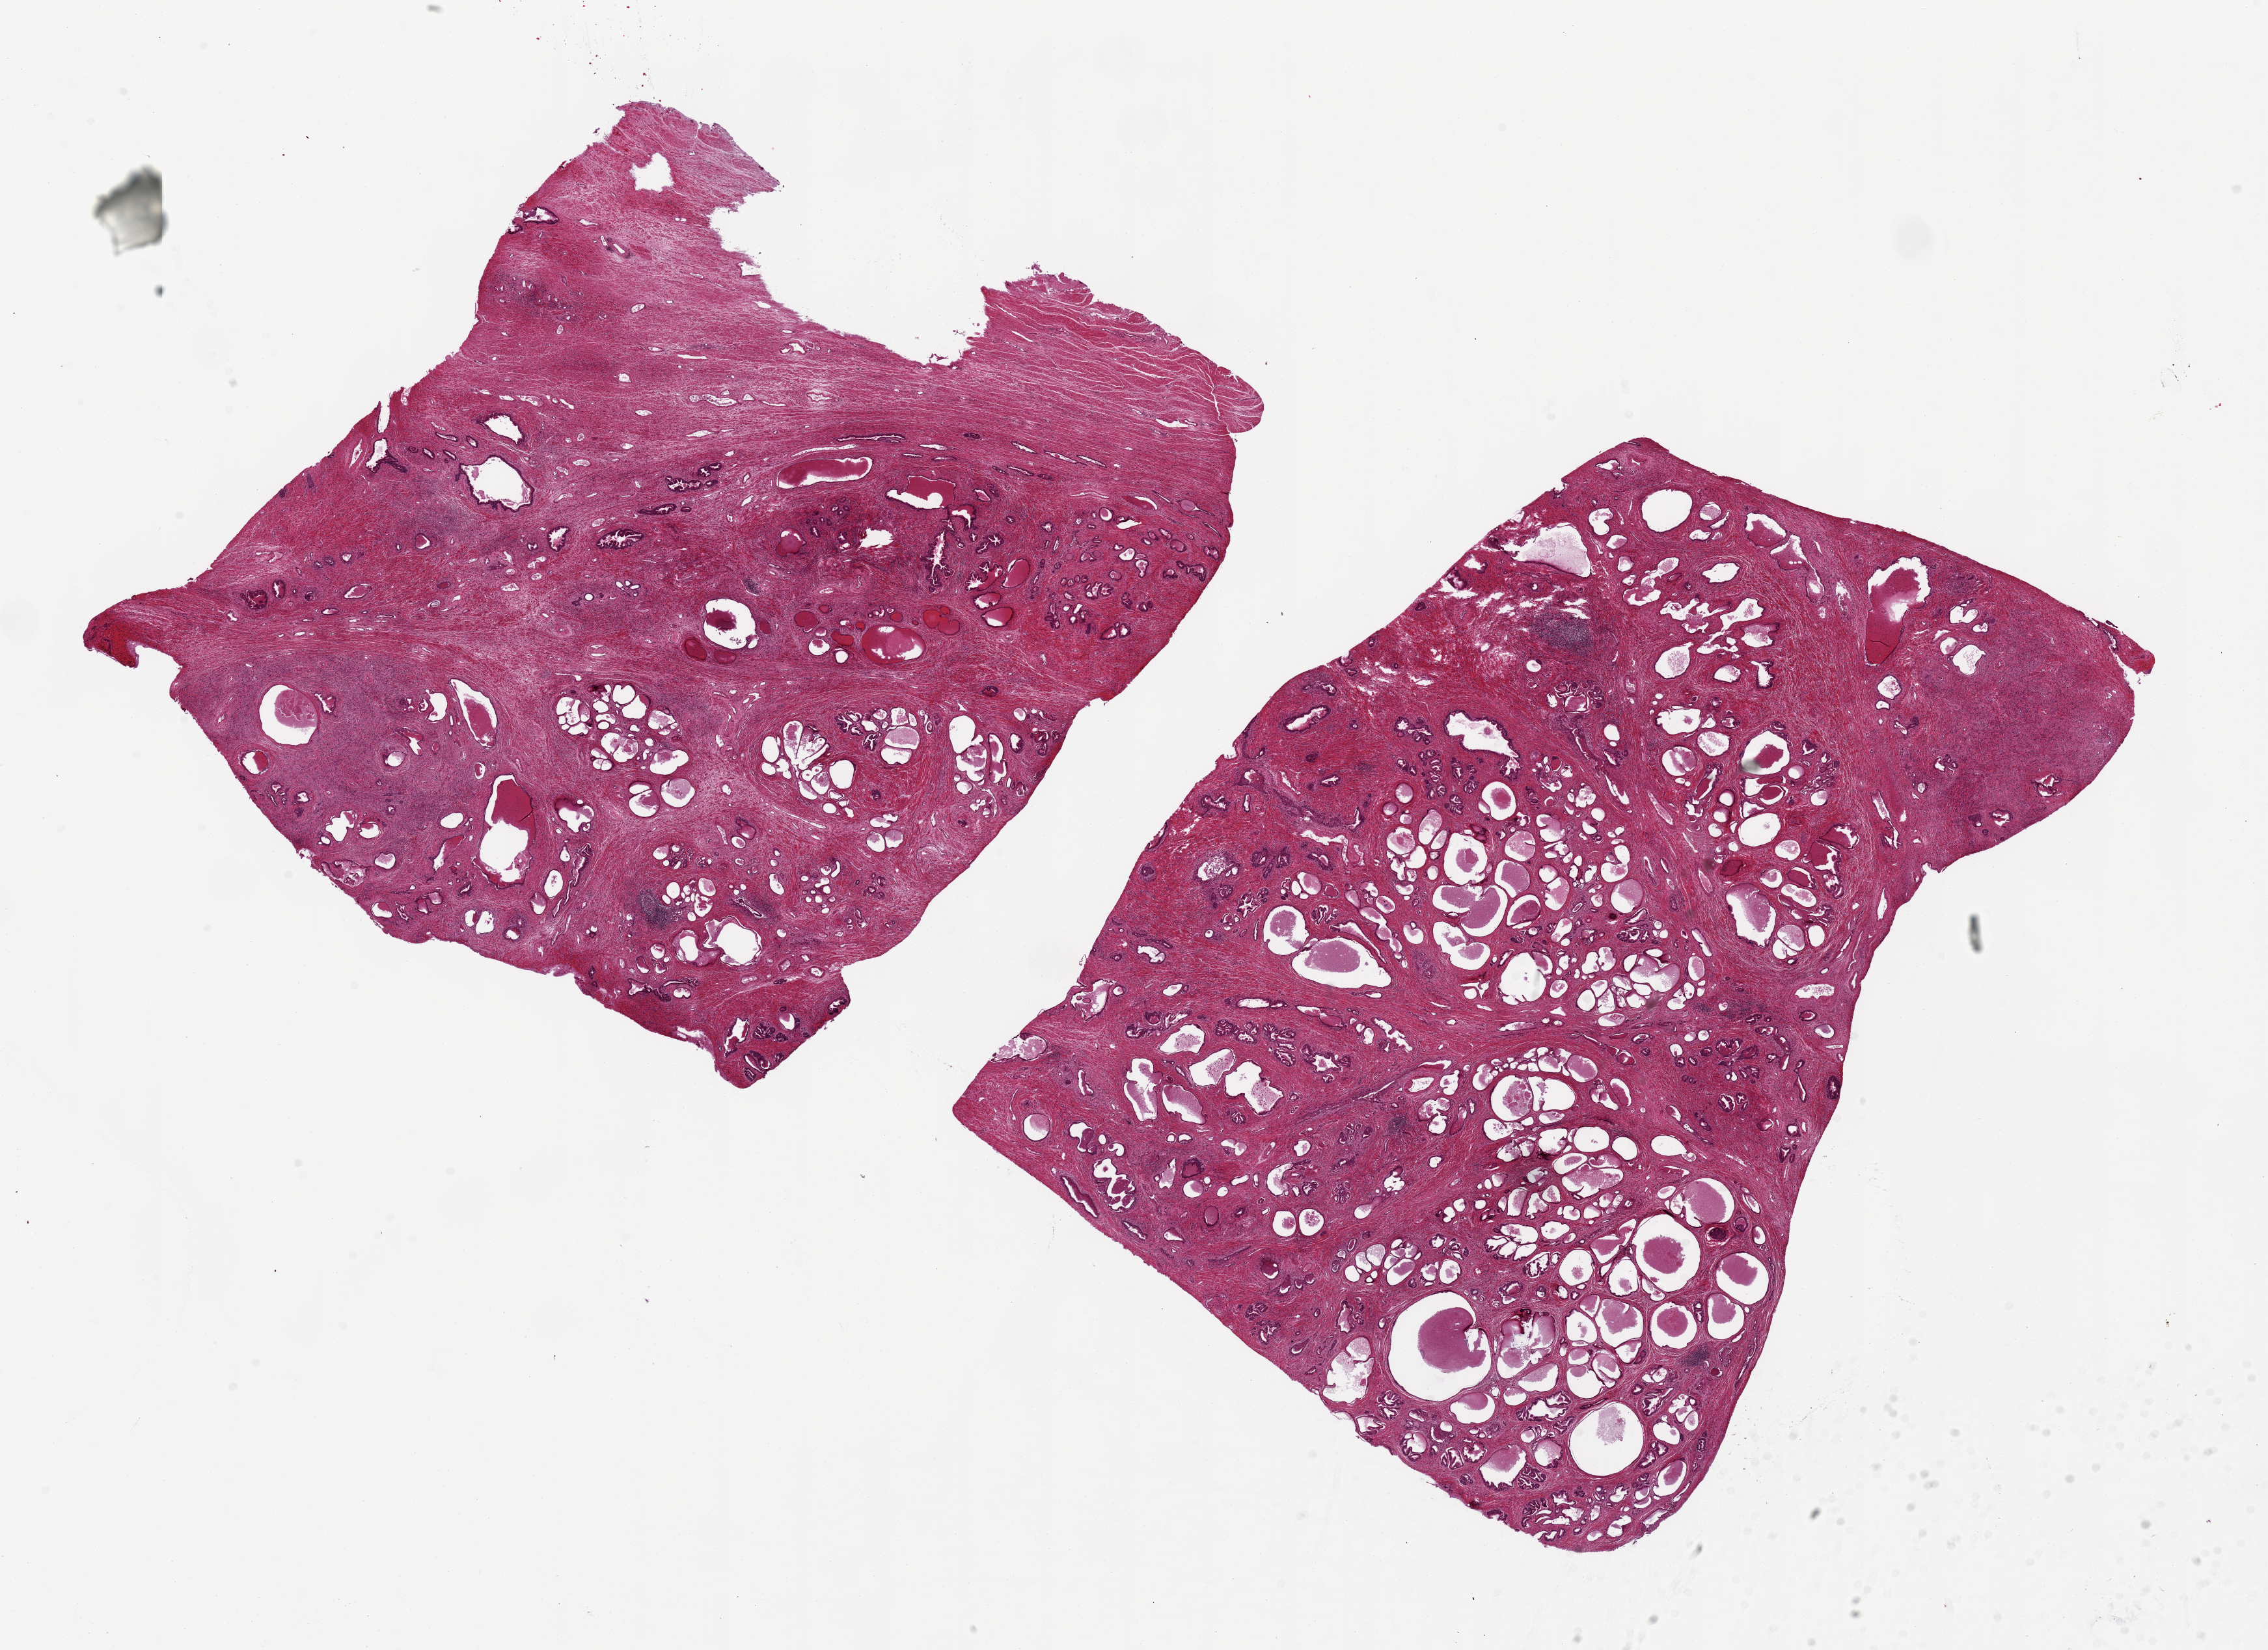
Whole-slide image, hematoxylin and eosin (H&E) stain — a low-resolution overview of the entire scanned area, about 27.6 x 20.1 mm (slide scanned at 20x), PAXgene-fixed paraffin-embedded (PFPE) section, target tissue: prostate, donor tissue sample. Donor: male.
Pathologist's review note for this sample: 2 ~11x8.5mm aliquots. Diffuse cystic glandular atrophy and patchy chronic prostatits.